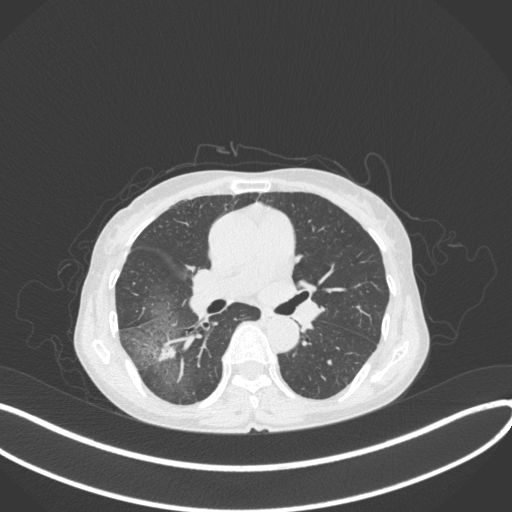
Chest CT, one axial slice. Lung window (W 1500 / L -600 HU). 1 mm slice thickness. 512 × 512 image matrix, field of view 400 × 400 mm. Patient: female, 69 years. From the clinical record (not read from this slice): clinical TNM (as recorded): T1b N0 M0.
Annotated regions visible in this slice (bounding box drawn by a radiologist):
- lung tumour (recorded histology: adenocarcinoma): bounding box <152,339,187,364> (left, top, right, bottom; pixels)